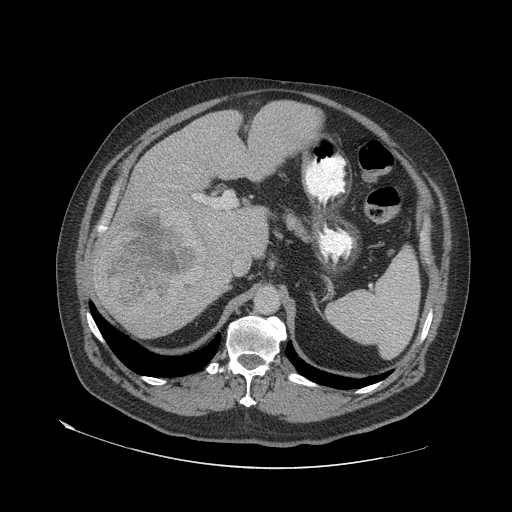
Contrast-enhanced abdominal CT (liver protocol), one axial slice. Position 40 of 79 along the scan axis. Soft-tissue window (W 400 / L 40 HU). 2.5 mm slice thickness. 512 × 512 image matrix, field of view 480 × 480 mm. Case-level facts recorded for this patient, not image findings: diagnosis: hepatocellular carcinoma (patient treated with transarterial chemoembolisation; whether this scan precedes or follows treatment is not stated here); TNM stage (as recorded): Stage-IVA; Child-Pugh class: A; tumour differentiation: well differentiated.
Annotated regions visible in this slice (semi-automatically segmented with operator editing):
- liver parenchyma outside the tumour (the mass and vessels are separate outlines, so this box may not span the whole liver): bounding box <92,100,322,337> (left, top, right, bottom; pixels)
- mass: <94,205,205,320>
- liver vessels: <101,195,199,232>